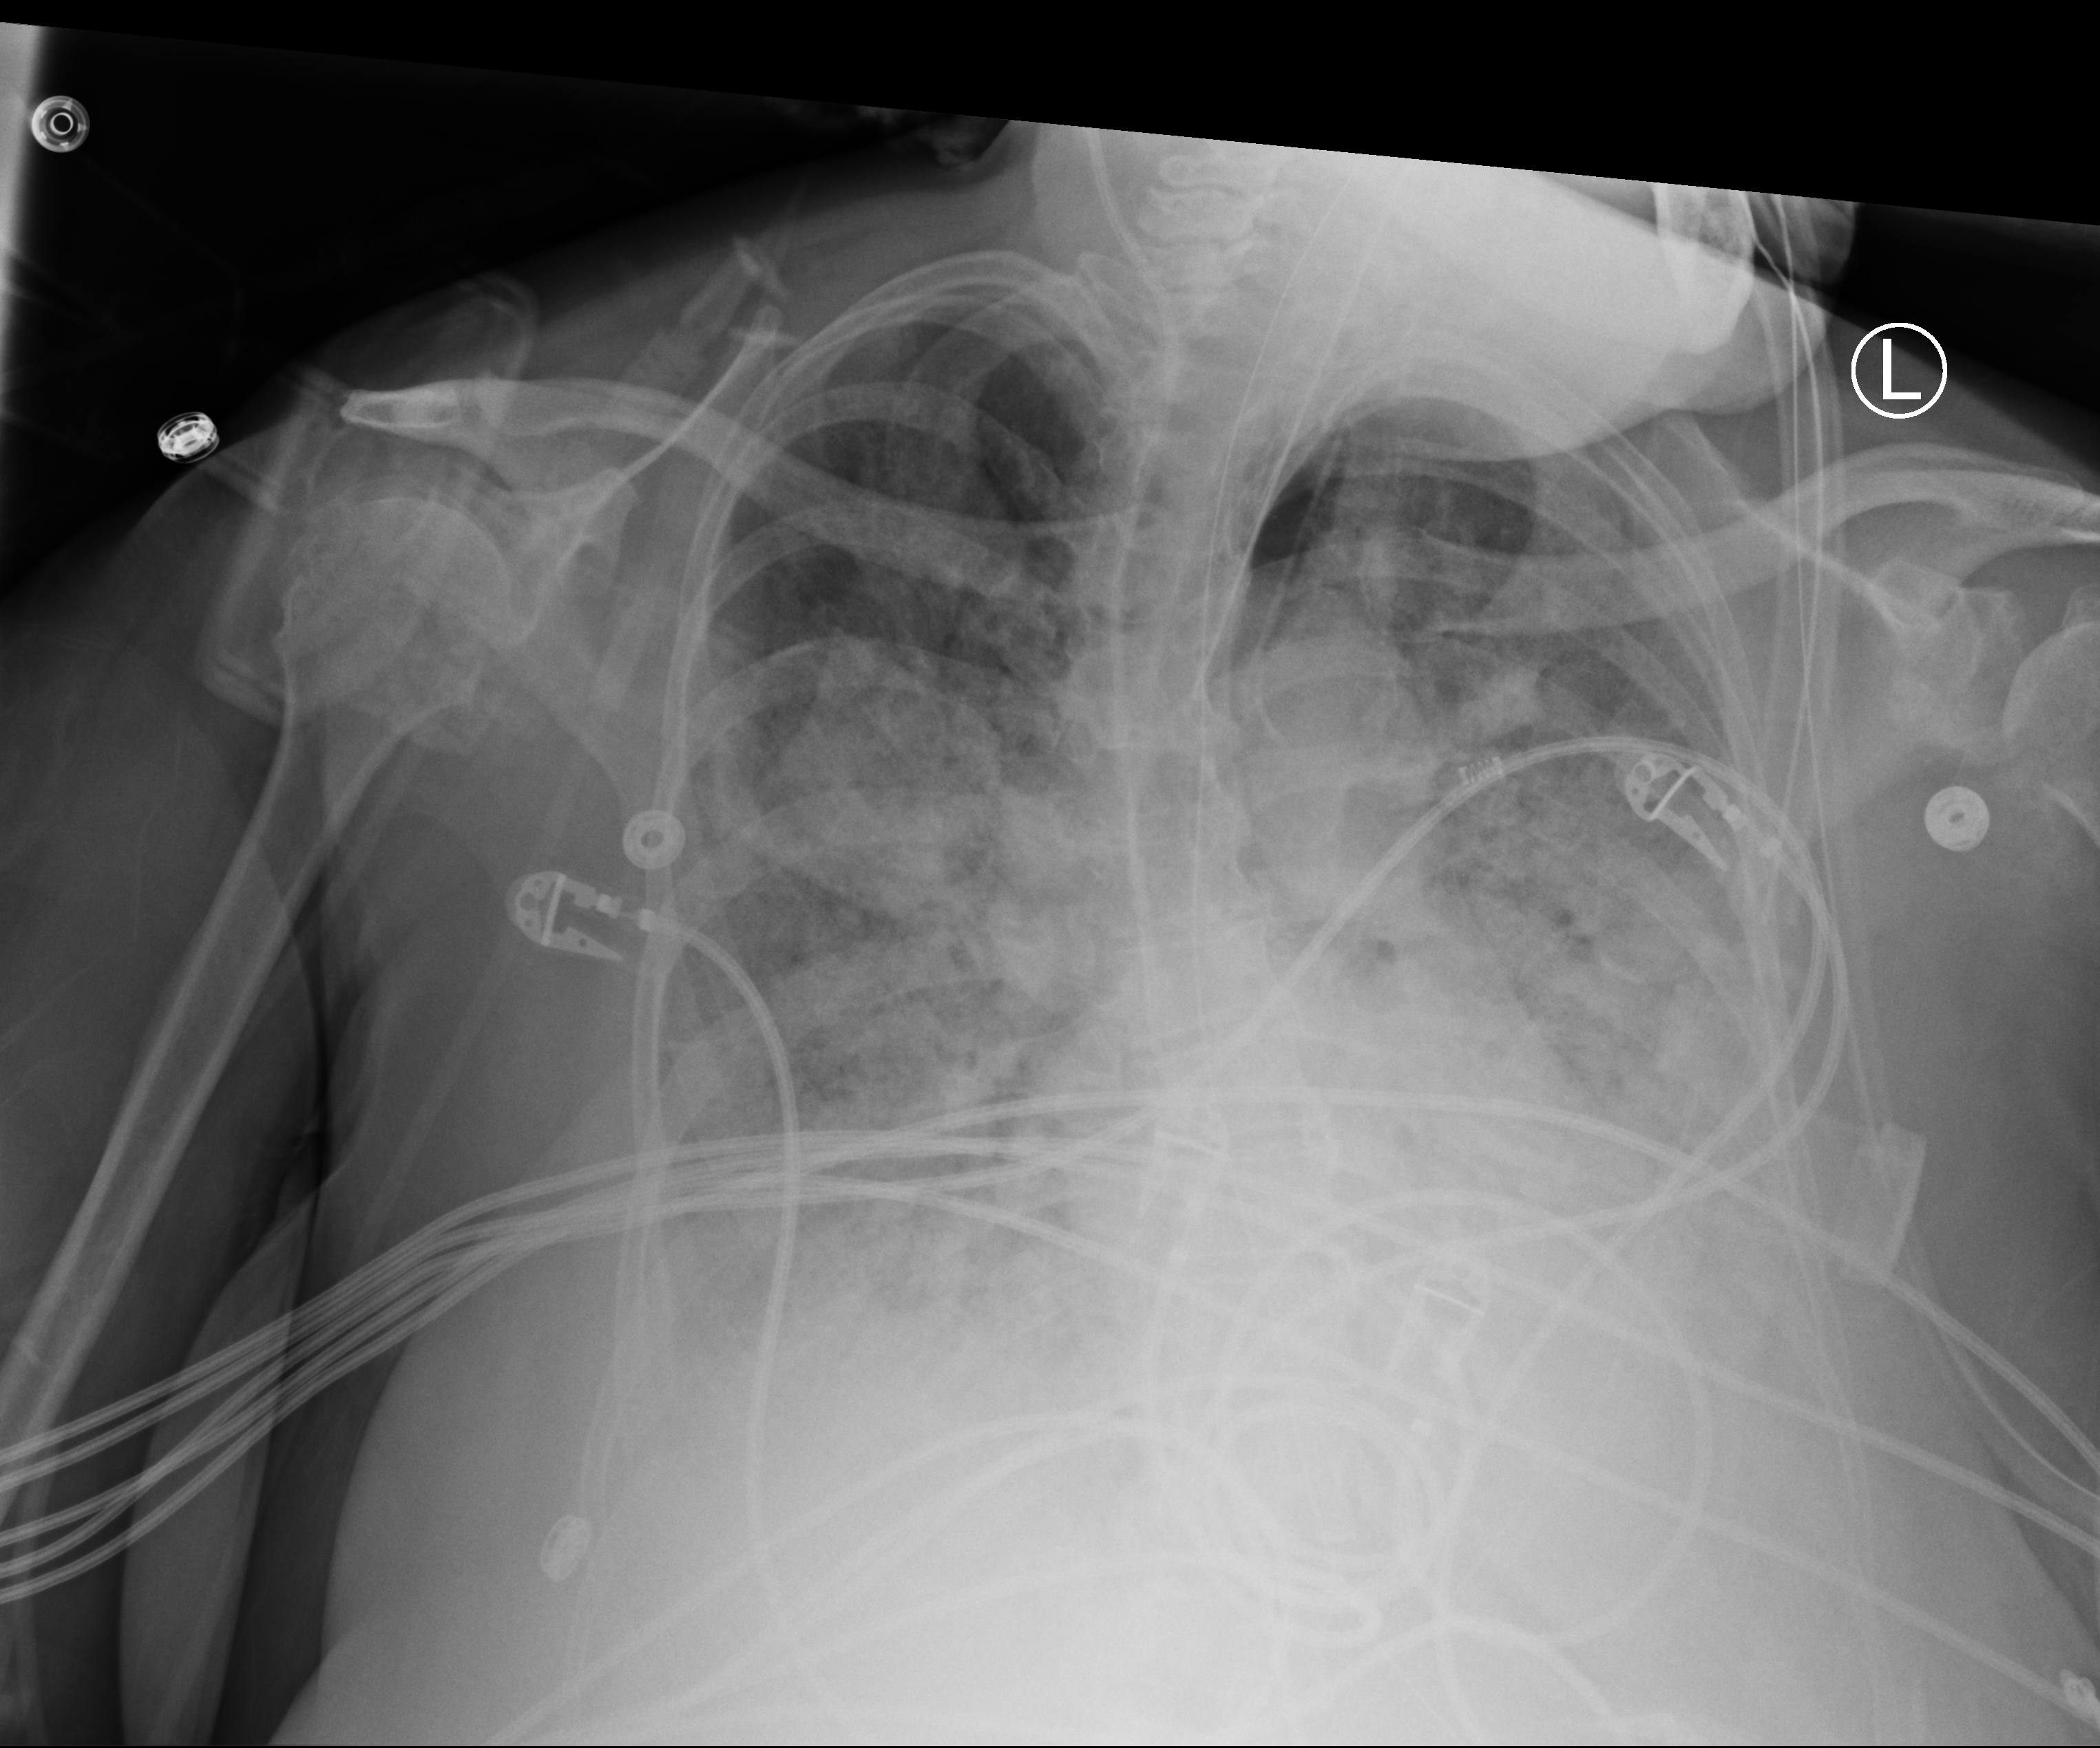
Chest X-ray (portable); anteroposterior (AP) projection. Female patient hospitalised with COVID-19, age 60–74 years.
Admission-level facts for this patient (not findings on this image; timing relative to this image not recorded):
- COPD (admission record): no